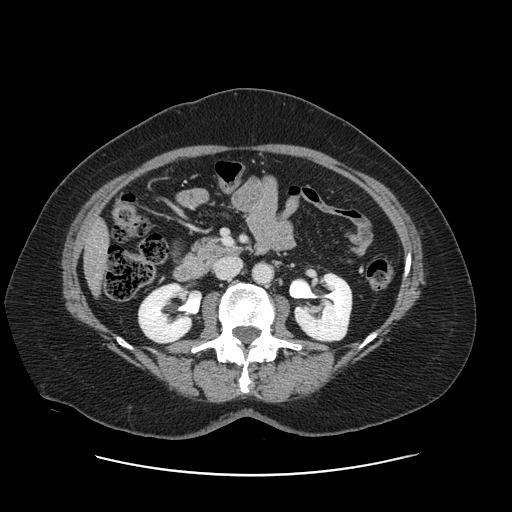
Contrast-enhanced abdominal CT, one axial slice; position 48 of 161 along the scan axis; 120 kVp; soft-tissue window (W 400 / L 40 HU); 2.5 mm slice thickness; 512 × 512 image matrix, field of view 398 × 398 mm. Female patient, age 62 years. Case-level facts recorded for this patient, not image findings: diagnosis: colorectal cancer liver metastases, imaged before liver resection; multiple liver metastases: no; largest metastasis: 2.5 cm; disease in both lobes: no.
Structures marked on this image (expert manual segmentation):
- liver: bounding box [x1, y1, x2, y2] px = [86, 223, 108, 291]